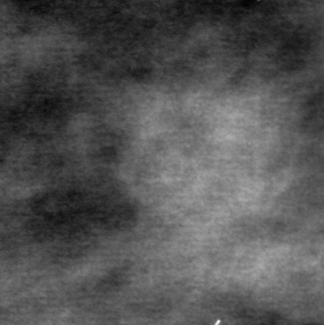
Crop from a digitized film mammogram around one marked abnormality; right breast; MLO view.
Marked abnormality: mass, shape irregular, margins ill defined; BI-RADS assessment category 0 (incomplete: needs additional imaging); subtlety rating 4 on a 1 (subtle) to 5 (obvious) scale; pathology (as recorded): malignant.